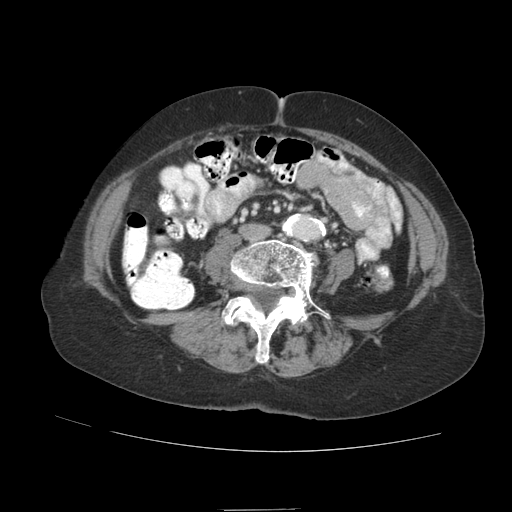
Contrast-enhanced abdominal CT (liver protocol), one axial slice; position 4 of 89 along the scan axis; reconstruction kernel STANDARD; soft-tissue window (W 400 / L 40 HU); 2.5 mm slice thickness; 512 × 512 image matrix. From the clinical record (not read from this slice): diagnosis: hepatocellular carcinoma (patient treated with transarterial chemoembolisation; whether this scan precedes or follows treatment is not stated here); TNM stage (as recorded): Stage-II.
Annotated regions visible in this slice (semi-automatic segmentation, software-assisted and operator-edited):
- liver parenchyma outside the tumour (the mass and vessels are separate outlines, so this box may not span the whole liver): bounding box <124,231,146,257> (left, top, right, bottom; pixels)
- liver vessels: <124,230,146,257>